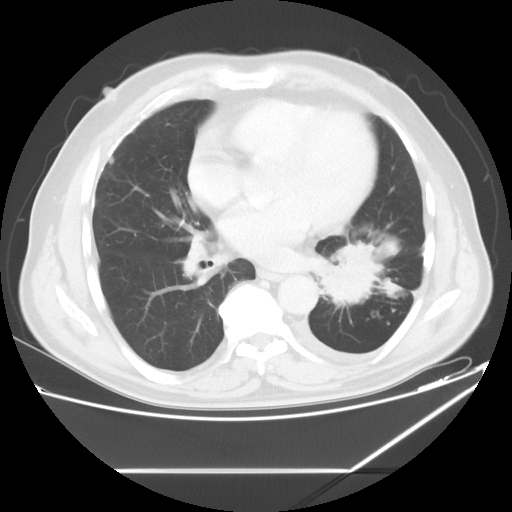
Chest CT, one axial slice; slice 27 of 60 in the series (ordered by position); reconstruction kernel STANDARD; lung window (W 1500 / L -600 HU); 5 mm slice thickness; 512 × 512 image matrix, field of view 395 × 395 mm. Patient: male, 62 years. From the clinical record (not read from this slice): clinical TNM (as recorded): T3 N0 M1.
Structures marked on this image (bounding box drawn by a radiologist):
- lung tumour (recorded histology: adenocarcinoma): bounding box [x1, y1, x2, y2] px = [321, 239, 384, 306]
- lung tumour (recorded histology: adenocarcinoma): [323, 241, 379, 306]